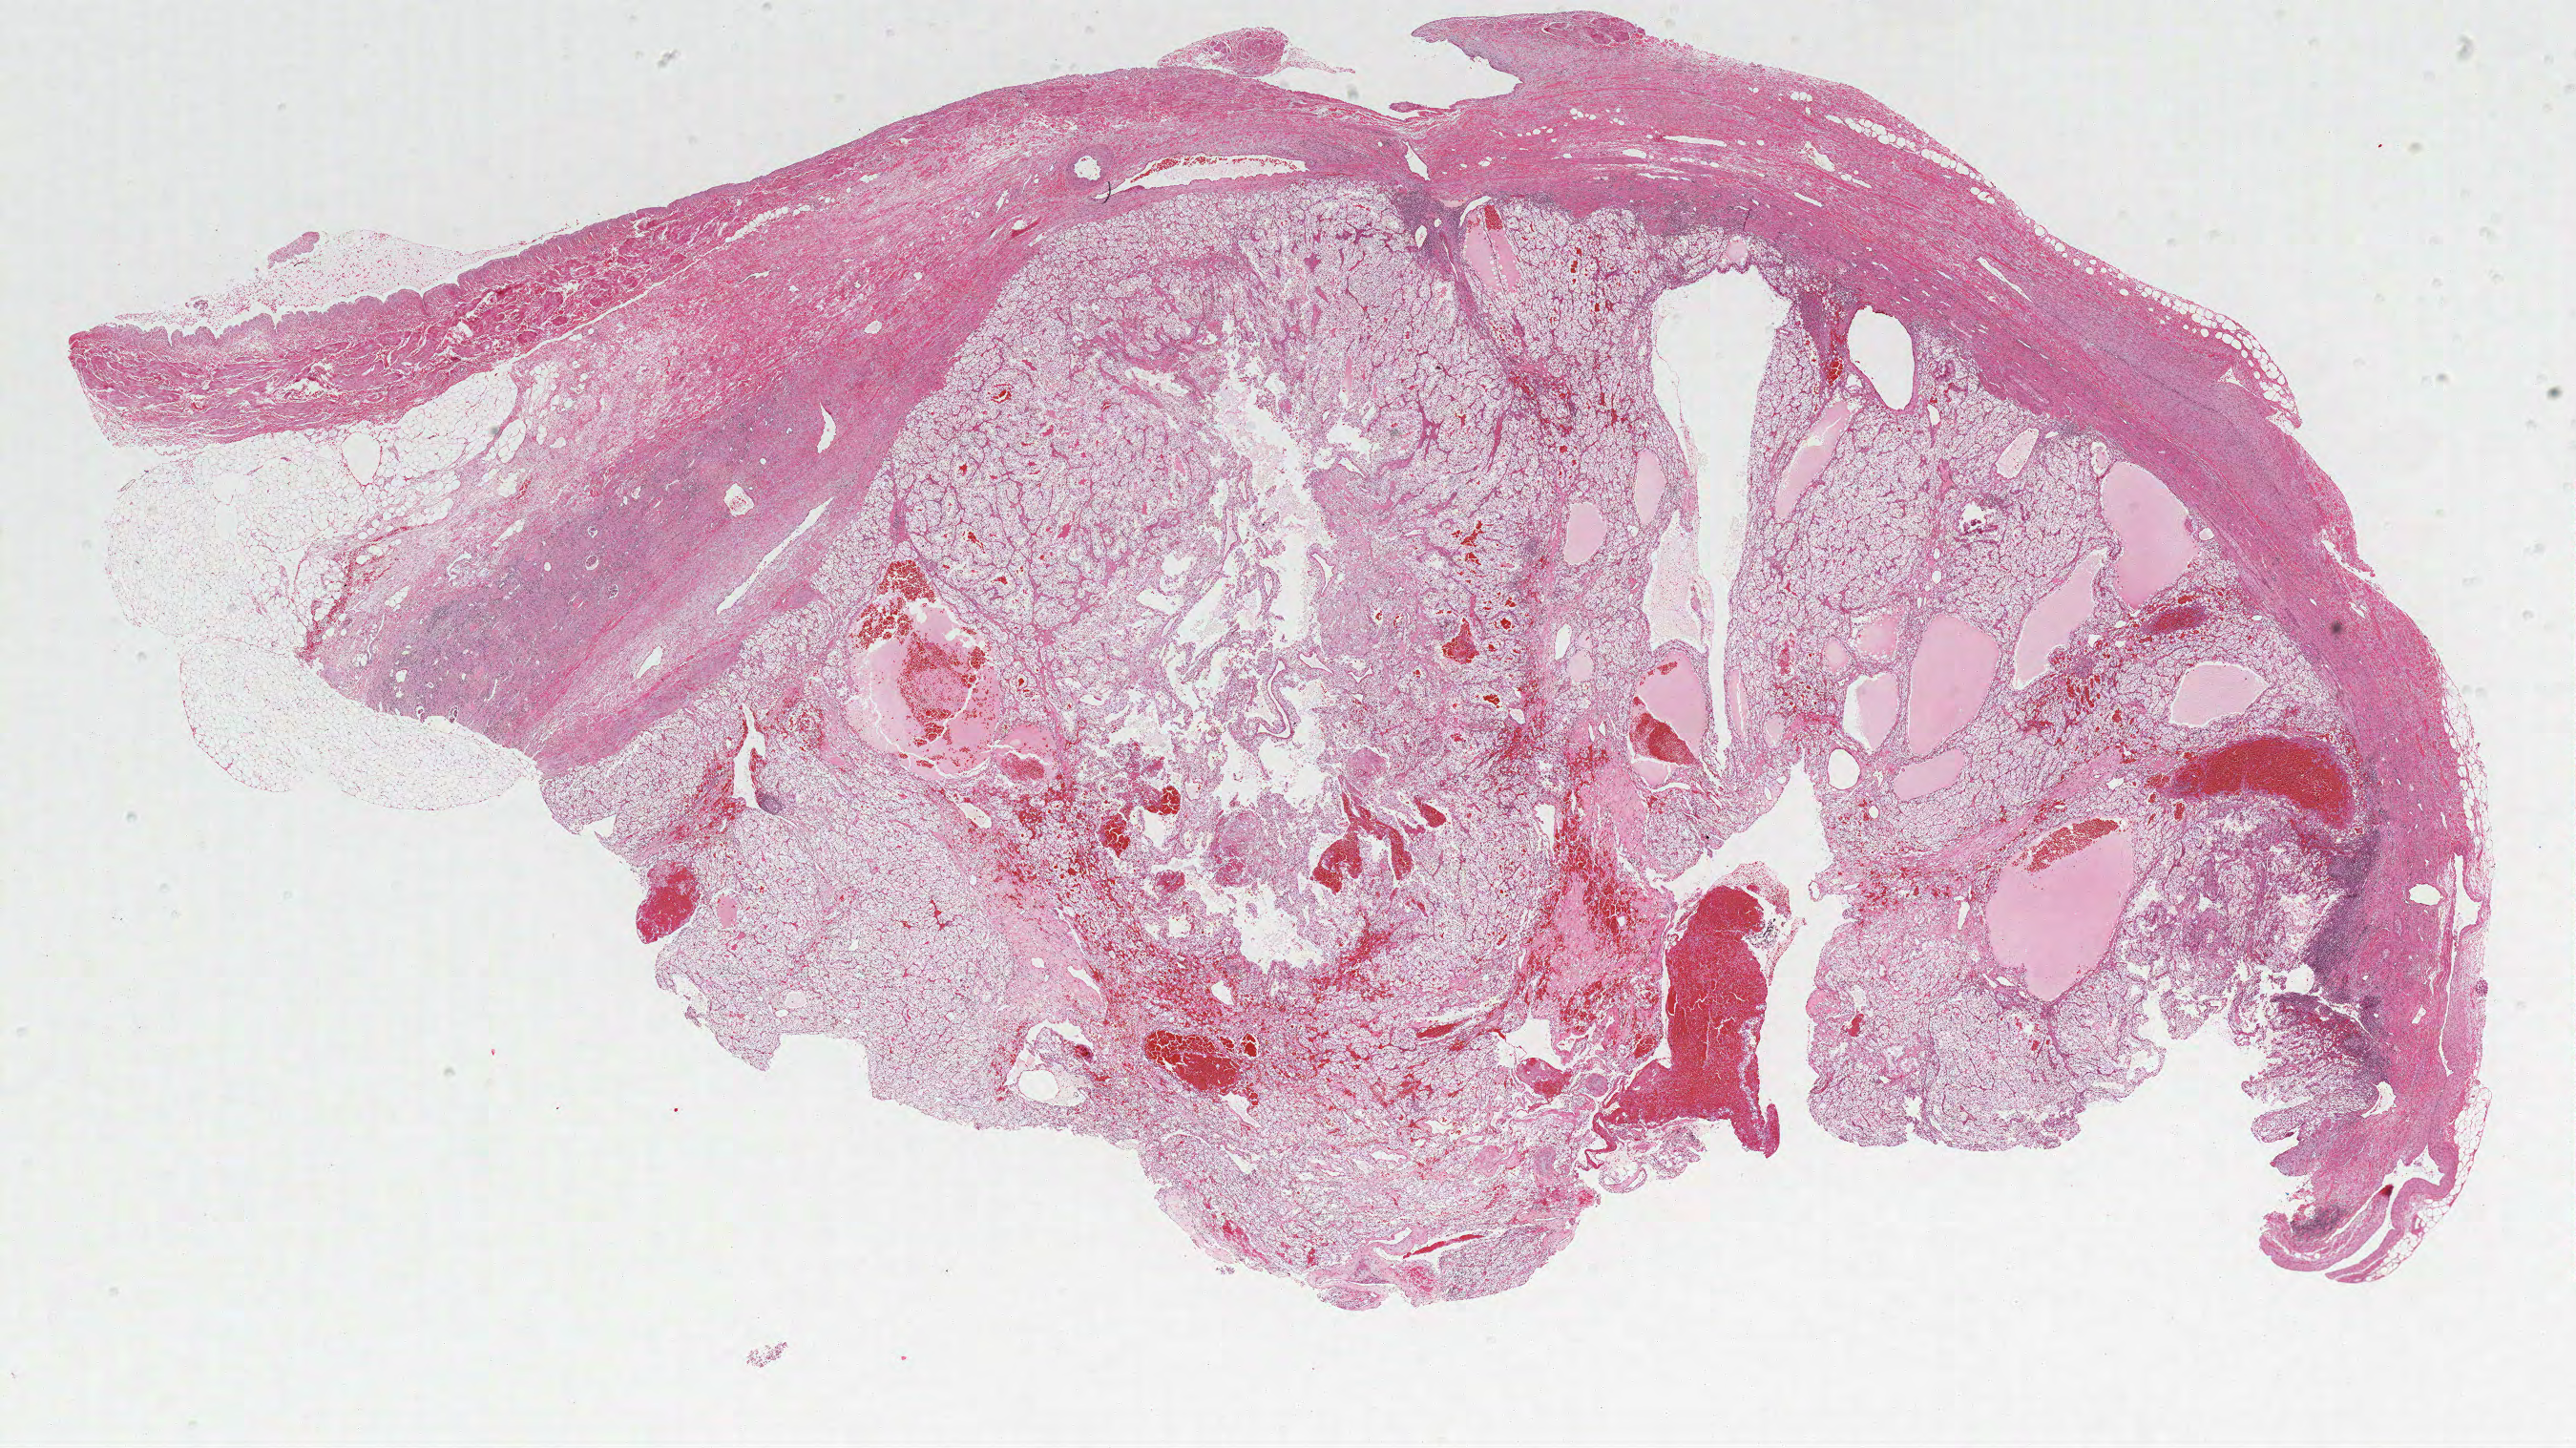
H&E whole-slide image, low-resolution overview of the scanned area, about 21.6 x 12.1 mm (from a 40x scan), FFPE section, primary tumour sample from the kidney. Female patient; age at initial diagnosis 54 years. Histologic grade: G2 (moderately differentiated).
Laterality: right. AJCC pathologic stage: I. Pathologic diagnosis: Clear cell adenocarcinoma, NOS. Lymph nodes positive (case pathology): 0 of 11 examined. TNM: T1a N0 M0.